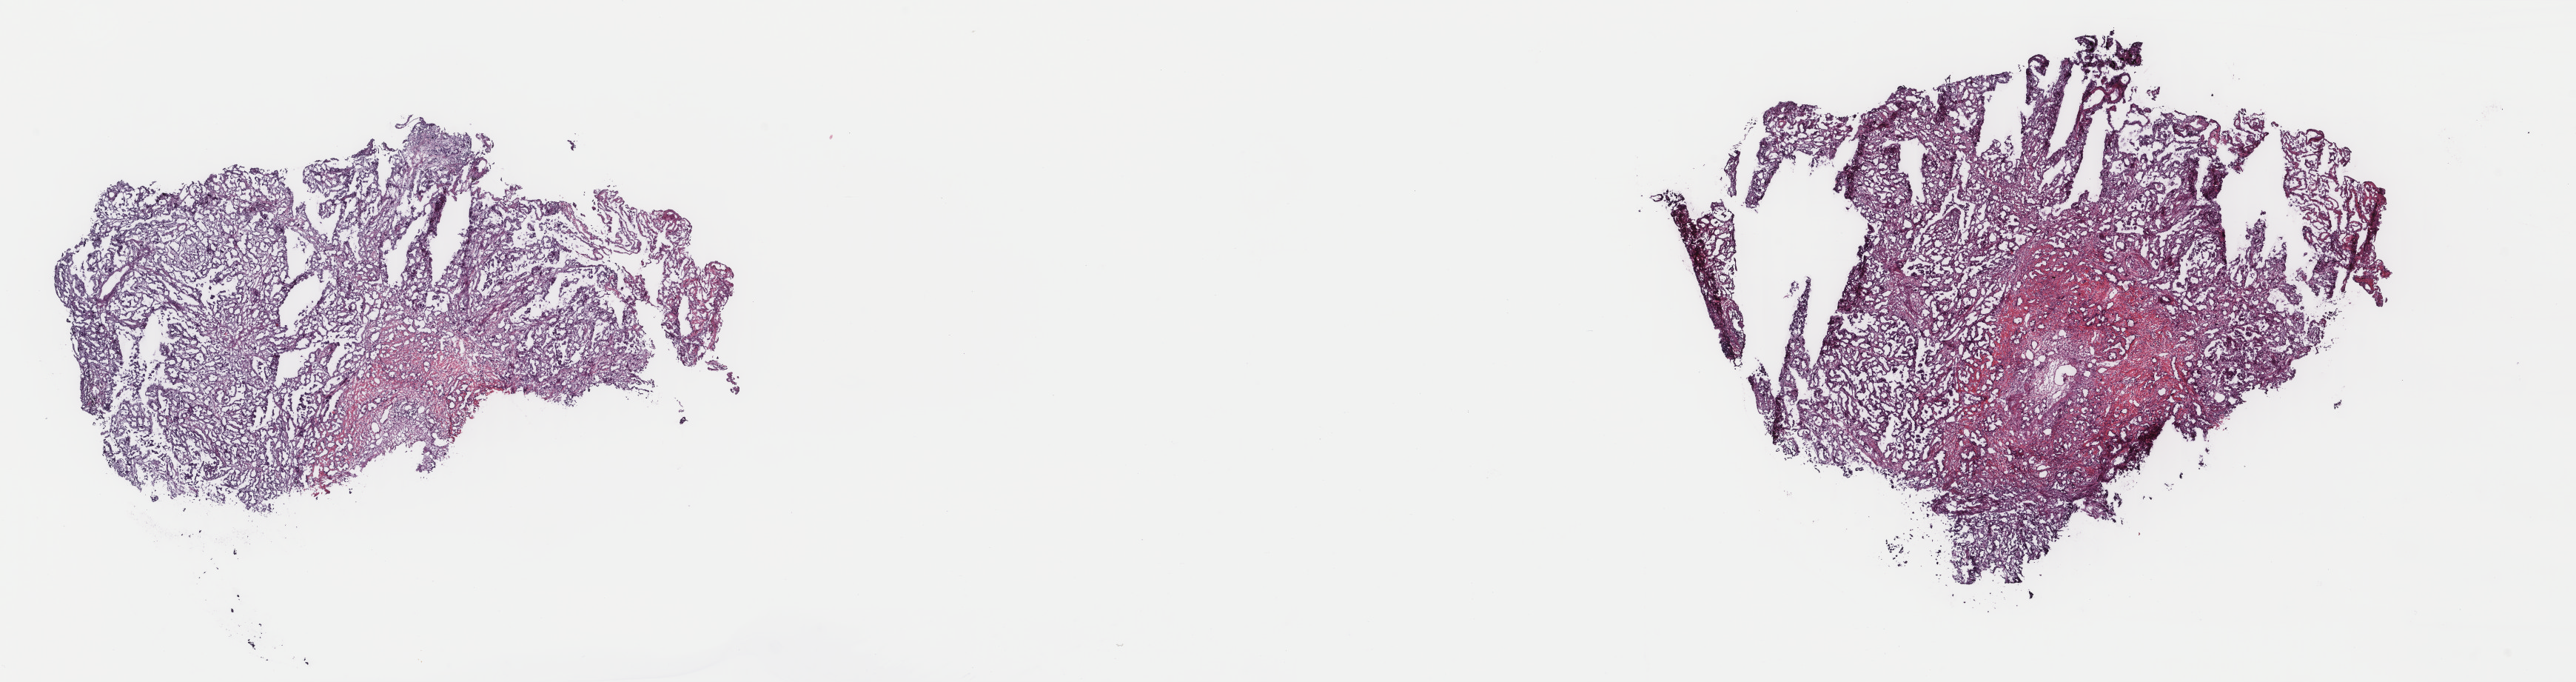
Whole-slide histology image, H&E, low-resolution overview of the scanned area, about 27.6 x 7.3 mm (from a 40x scan); frozen section from the top of the tissue portion; sample: primary tumour, lung. Female patient; age at initial diagnosis 87 years. Slide review estimates, as recorded: tumour cells 100%, tumour nuclei 65%, normal cells 0%, stromal cells 0%, necrosis 0%. Infiltration values recorded for this section: lymphocyte infiltration 3%, monocyte infiltration 3%, neutrophil infiltration 0%.
Diagnosis: Acinar cell carcinoma. AJCC pathologic stage: IIIA (6th edition).